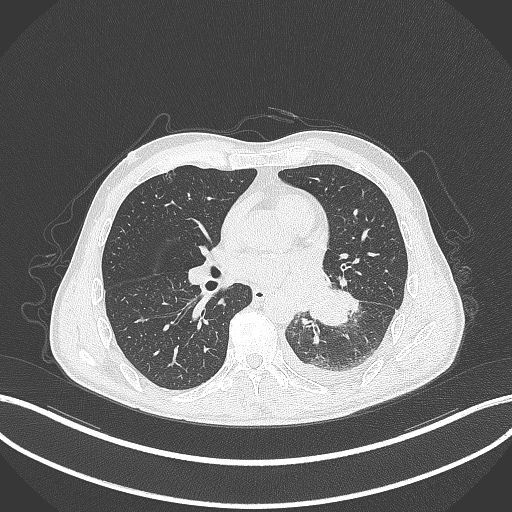
Chest CT, one axial slice. Position 152 of 295 along the scan axis. Reconstruction kernel B70f. 120 kVp. Lung window (W 1500 / L -600 HU). 1 mm slice thickness. 512 × 512 image matrix. Male patient, age 47 years. Case-level facts recorded for this patient, not image findings: clinical TNM (as recorded): T3 N1 M1c; histopathological grade: G3.
Annotated regions visible in this slice (rectangle marked by the reading radiologist):
- lung tumour (recorded histology: small cell carcinoma): bounding box (x1, y1, x2, y2) in pixels: (309, 289, 348, 327)